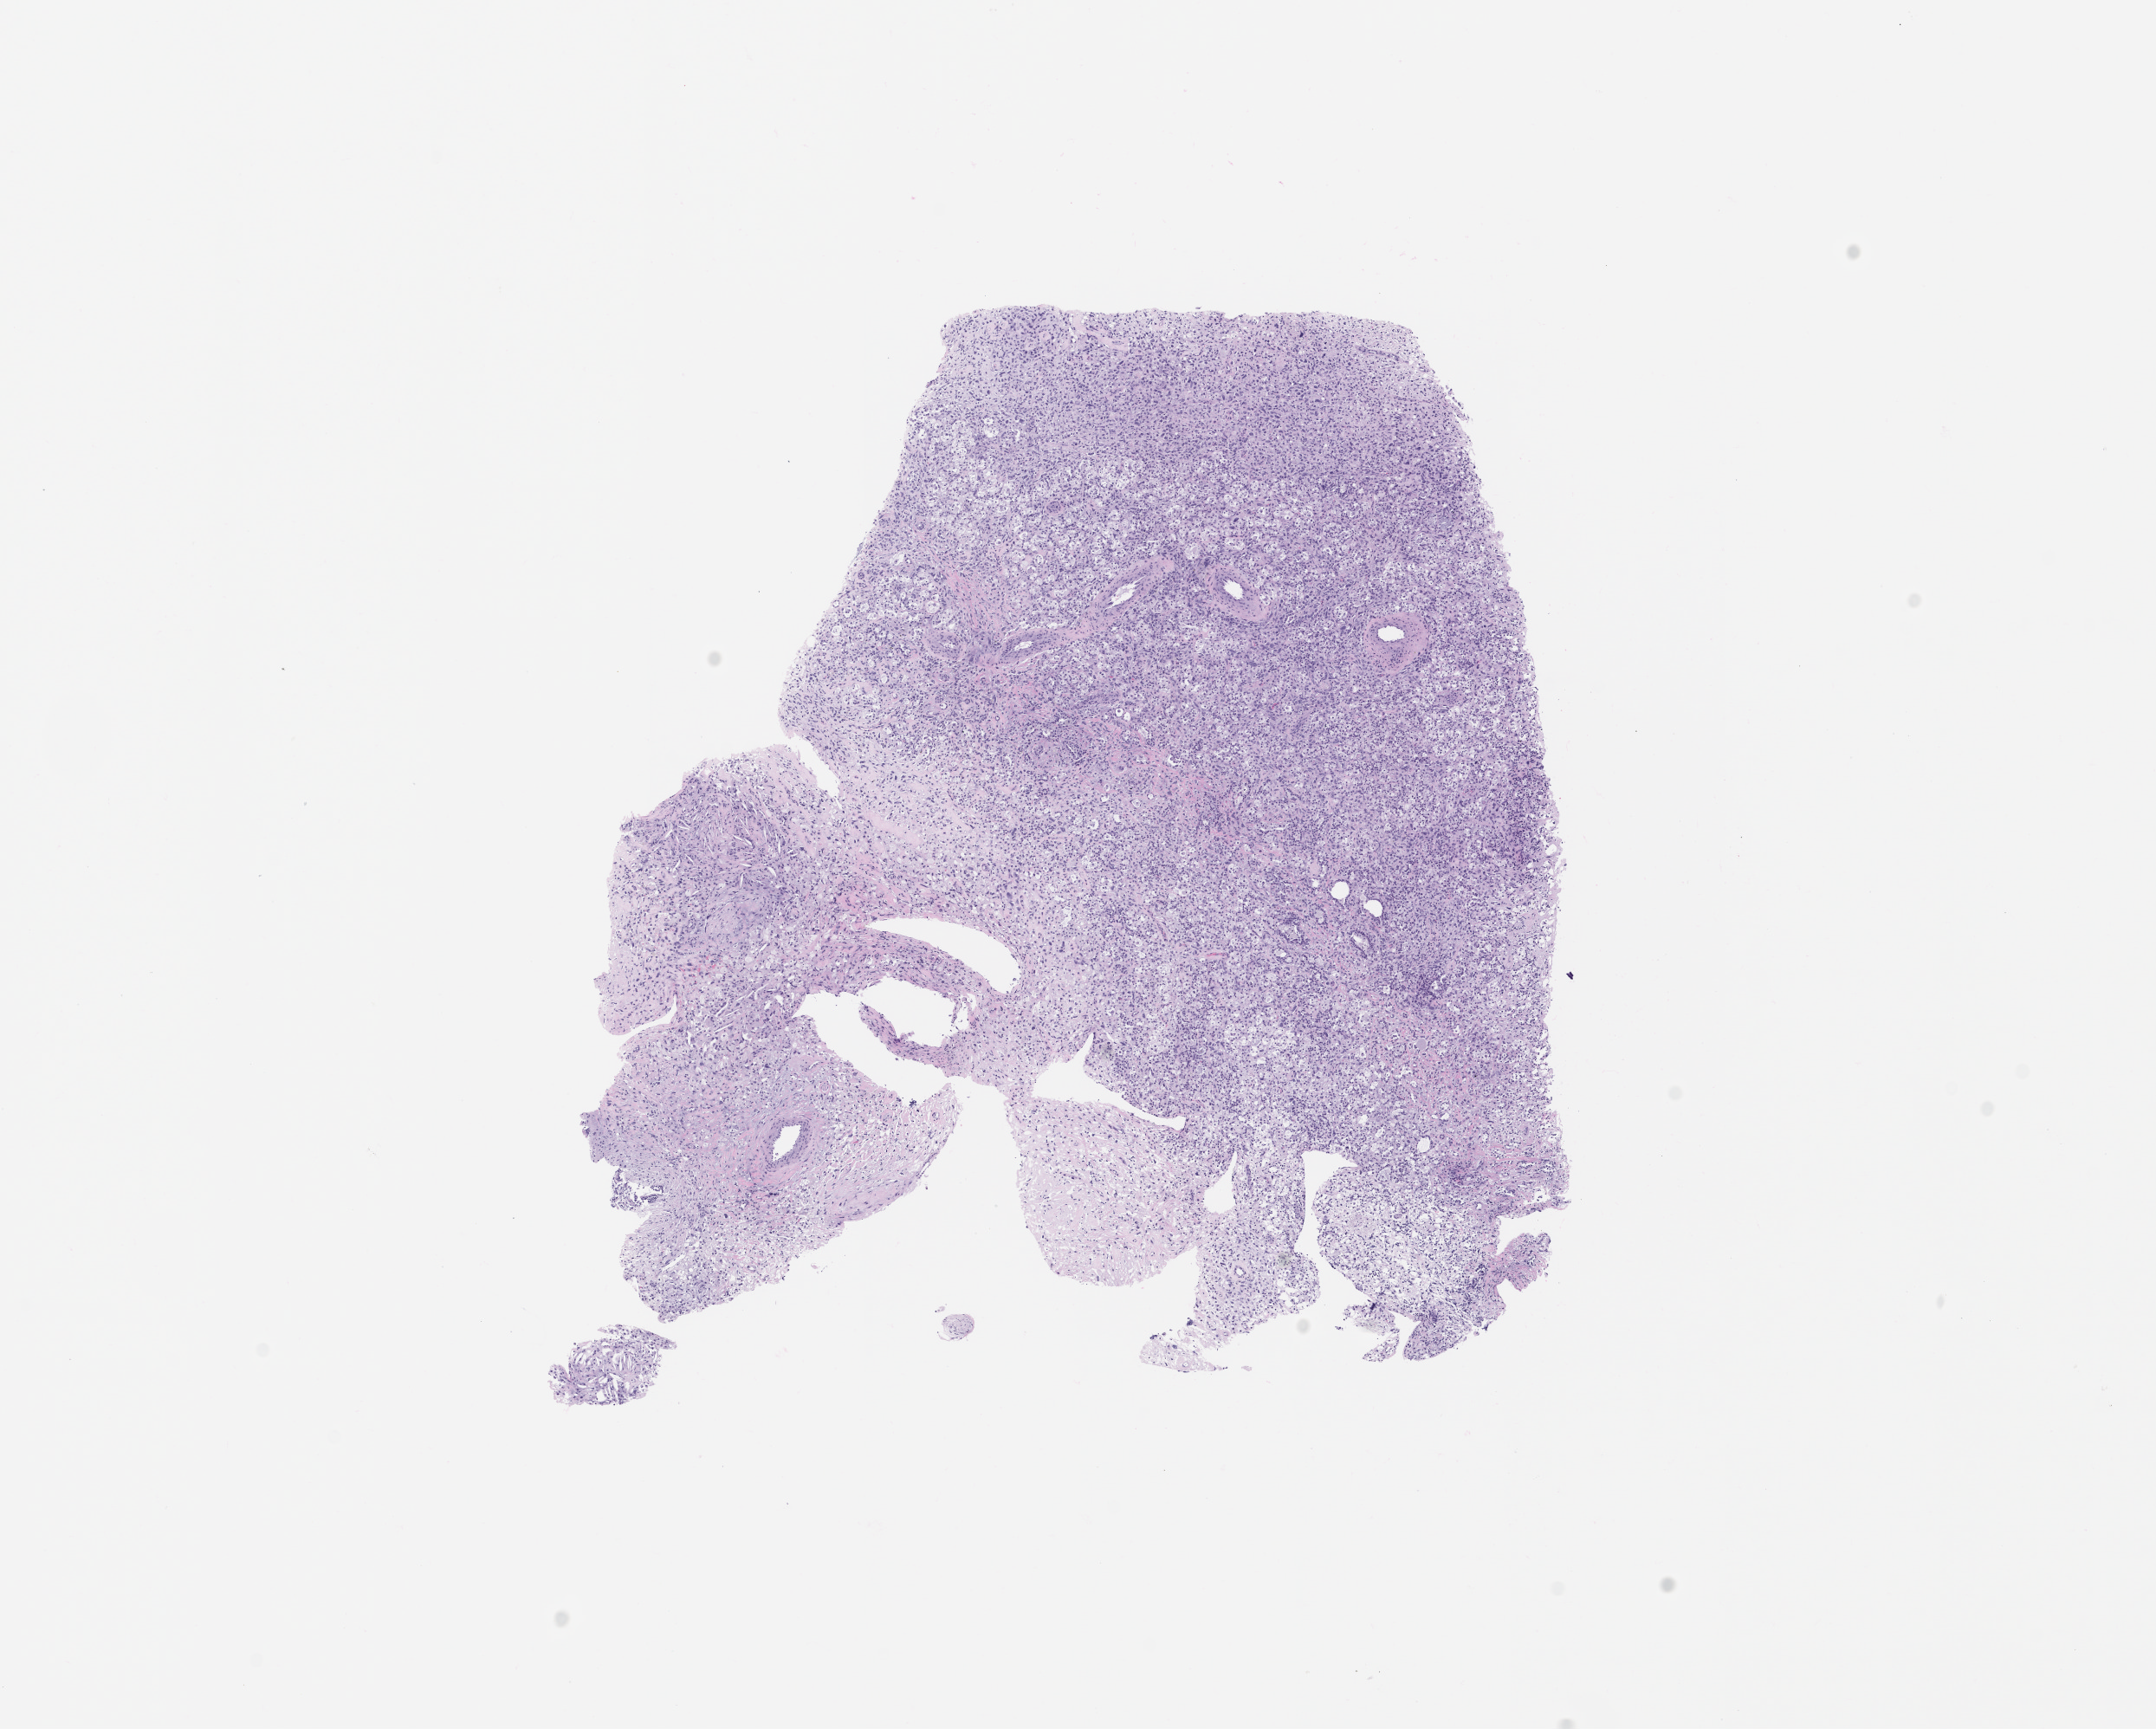
H&E whole-slide image of the patient's (originator) tumor tissue — whole scanned area (about 10.0 x 8.0 mm) shown as a low-resolution overview. Formalin-fixed paraffin-embedded section. Originating tumor site category: musculoskeletal. Patient: male, 18 years old.
Diagnosis: Synovial Sarcoma.